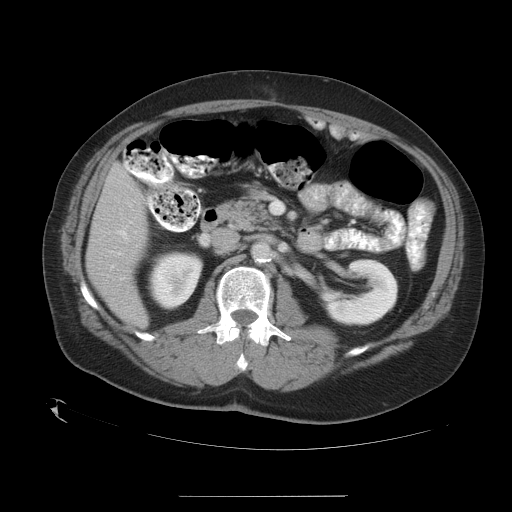
Contrast-enhanced abdominal CT, one axial slice; slice 13 of 35 in the series (ordered by position); 120 kVp; intravenous contrast given; soft-tissue window (W 400 / L 40 HU); 7.5 mm slice thickness; 512 × 512 image matrix, field of view 450 × 450 mm. Male patient, age 67 years. From the clinical record (not read from this slice): diagnosis: colorectal cancer liver metastases, imaged before liver resection; multiple liver metastases: no; largest metastasis: 2.3 cm; chemotherapy before resection: no.
Structures marked on this image (expert manual segmentation):
- liver: bounding box [x1, y1, x2, y2] px = [88, 167, 147, 324]
- planned liver remnant (the part of the liver to remain after resection): [88, 167, 147, 324]
- portal vein (with intrahepatic branches): [118, 230, 136, 243]